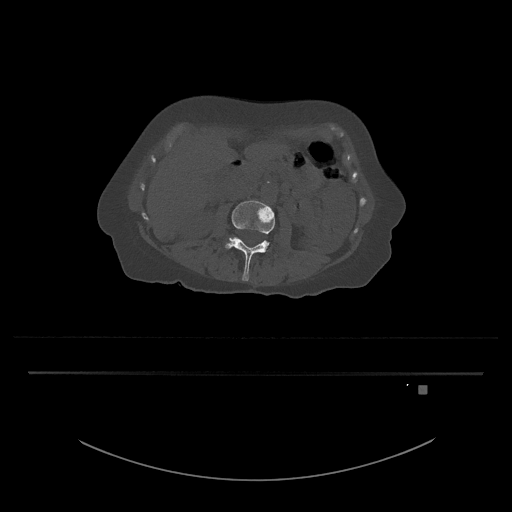
CT including the spine, one axial slice. Slice 423 of 797 in the series (ordered by position). 120 kVp. Bone window (W 1800 / L 400 HU). 0.5 mm slice thickness. 512 × 512 image matrix, field of view 500 × 500 mm. Female patient, age 57 years. From the clinical record (not read from this slice): primary cancer: cervical.
Annotated regions visible in this slice (semi-automatic segmentation, software-assisted and operator-edited):
- L3 vertebra: box from (x=225, y=200) to (x=275, y=281) px